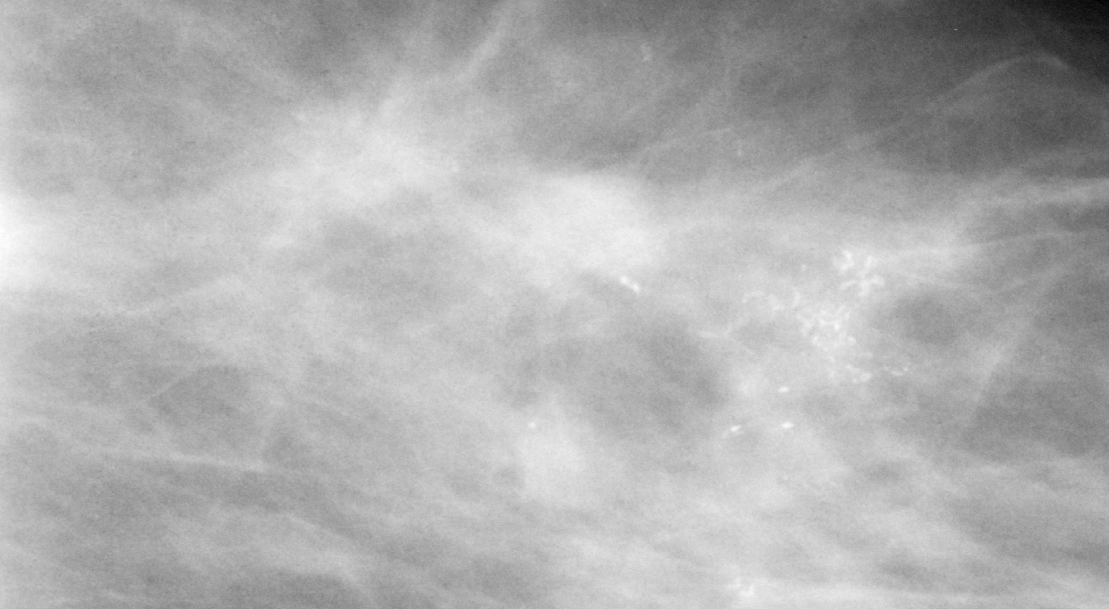
Region of interest cut from a scanned film mammogram (one marked finding), left breast, CC view.
- Marked abnormality: calcifications, morphology pleomorphic, distribution clustered; BI-RADS assessment category 5; pathology (as recorded): malignant.